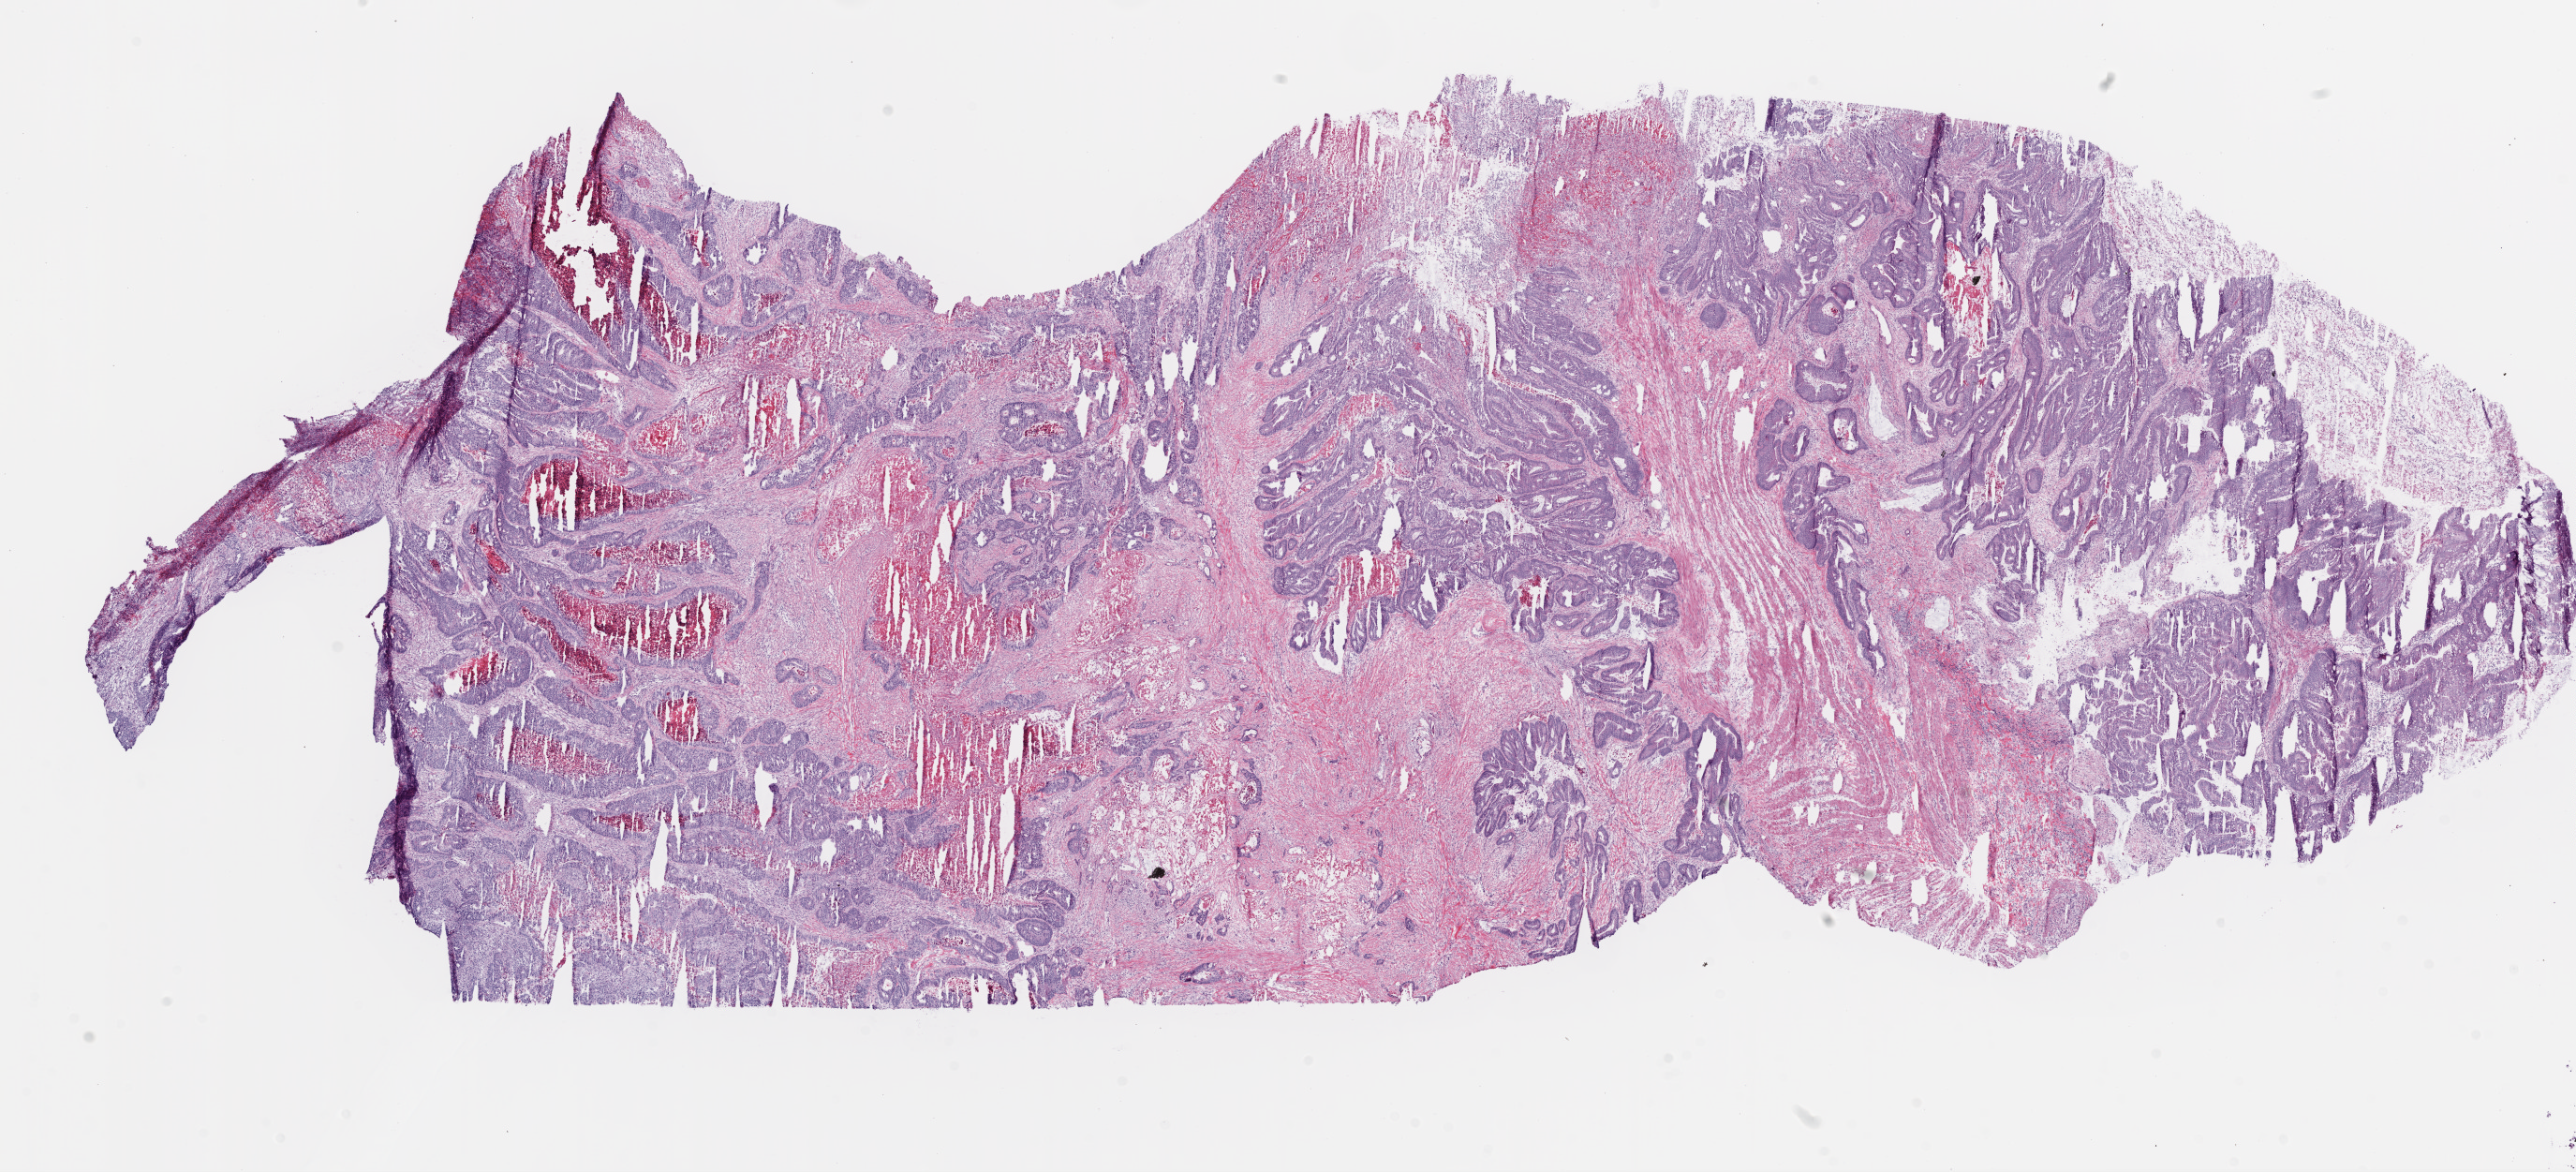
Whole-slide histology image, Hematoxylin and eosin (H&E) stained, low-resolution overview of the scanned area, about 22.1 x 10.0 mm, frozen section, primary tumour sample from the colon. Male, age 70 years at initial diagnosis. Composition of this section per pathologist review: tumour cells 70%, tumour nuclei 80%, normal cells 0%, stromal cells 20%, necrosis 10%.
AJCC pathologic stage: IV (6th edition). Diagnosis: Adenocarcinoma, NOS. Lymph nodes positive (case pathology): 2 of 13 examined.